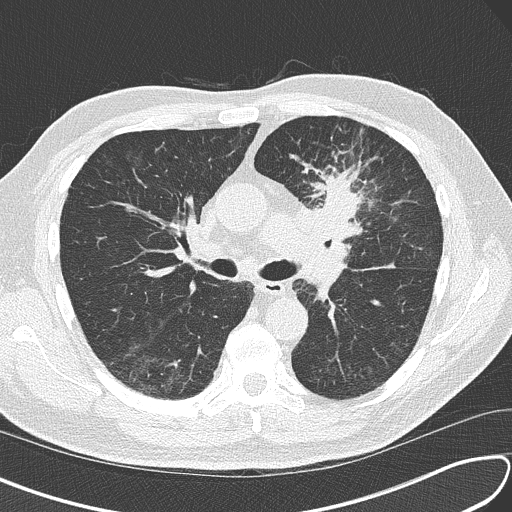
Low-dose screening chest CT, axial slice; third screening round (two years after baseline); lung window (W 1500 / L -600 HU); lung (sharp) reconstruction kernel (B50f); 512 × 512 image matrix. Male, age 67 years at enrolment.
• Lesion marked by an expert reader, box from (x=295, y=164) to (x=395, y=255) px.
• Reader record for this screening exam (exam-level; its link to the box is not recorded): non-calcified nodule or mass ≥4 mm, left upper lobe, 30 × 23 mm, soft tissue attenuation, pre-existing on the prior screen: no.
• Official screen result: positive, other.
• Later outcome: lung cancer diagnosed 41 days after this screen — small cell carcinoma, NOS, left upper lobe, stage IV (AJCC 6th edition), 30 mm at pathology.